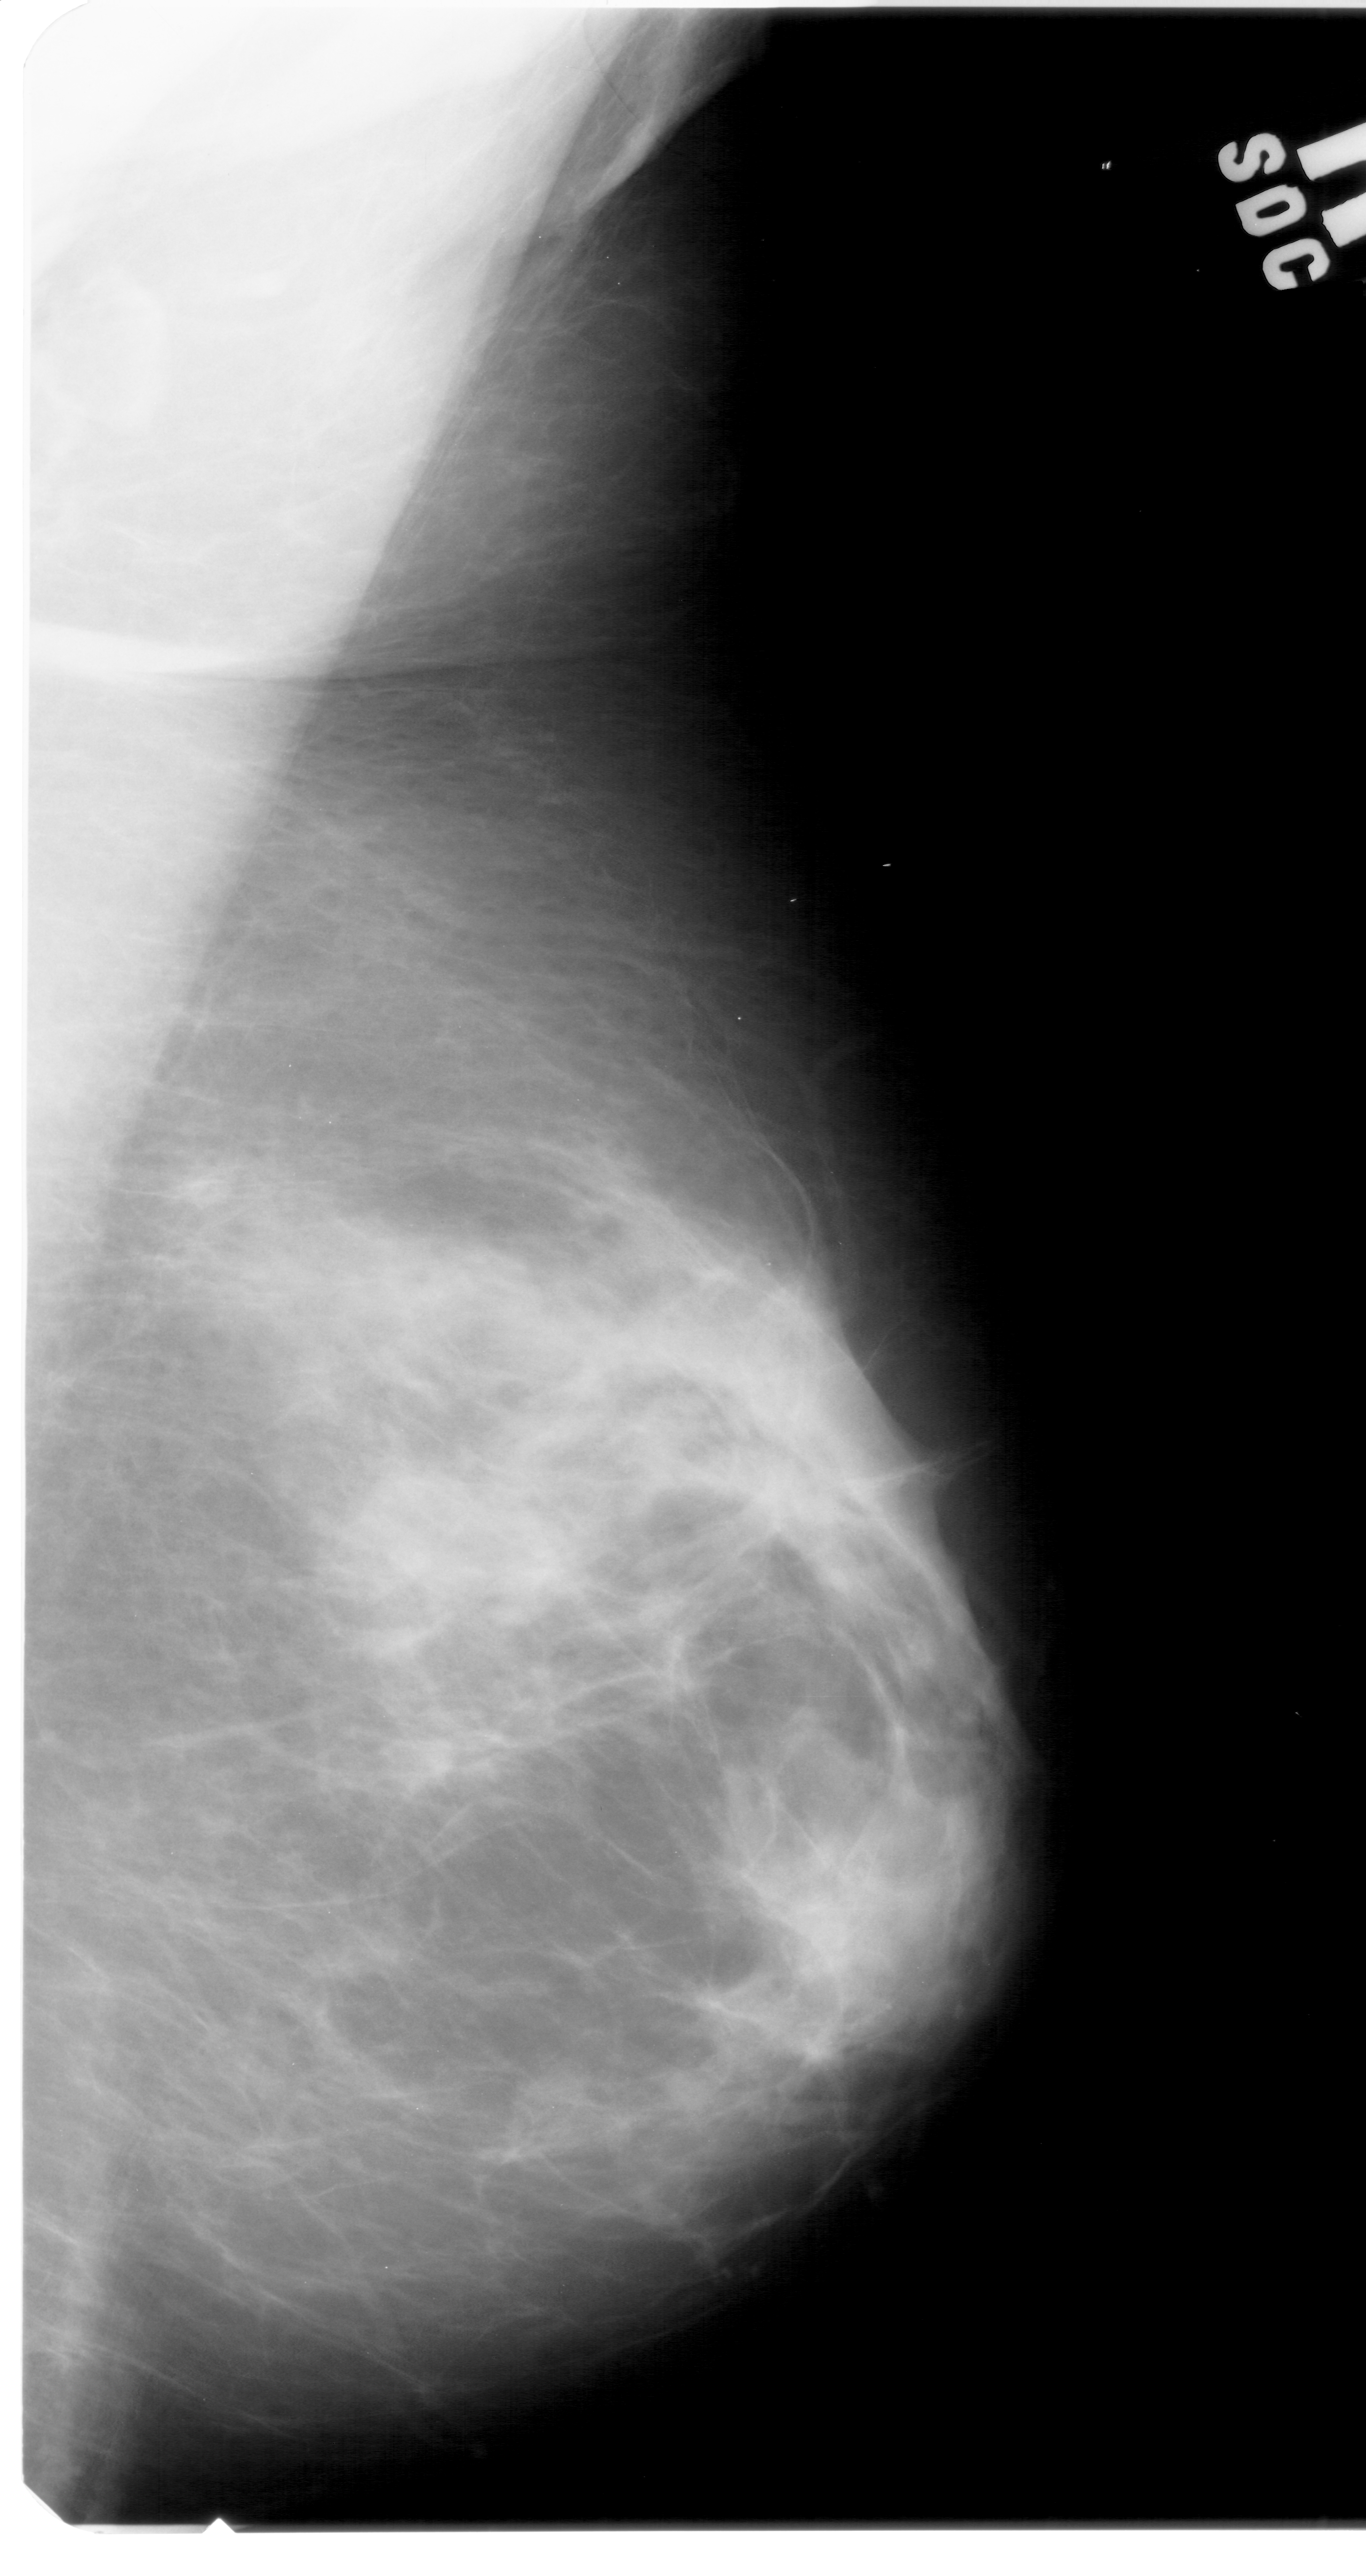
Digitized screen-film mammogram; right breast; mediolateral oblique (MLO) view; breast composition: extremely dense (BI-RADS density category 4 of 4); 1366 × 2576 image matrix.
Expert-marked regions of interest on this image (one box per marked abnormality):
- mass, shape irregular, margins spiculated; BI-RADS assessment category 5; pathology result (as recorded, not read from the image): malignant: bounding box <640,1351,927,1628> (left, top, right, bottom; pixels)